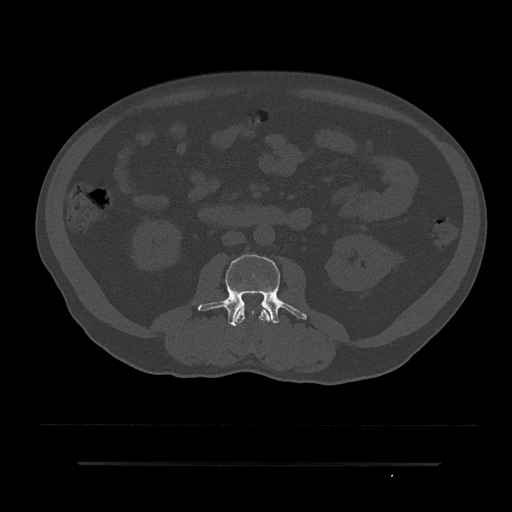
CT including the spine, one axial slice. Reconstruction kernel Br40s/3. 120 kVp. Bone window (W 1800 / L 400 HU). 0.5 mm slice thickness. 512 × 512 image matrix, field of view 464 × 464 mm. Male patient, age 59 years. Case-level facts recorded for this patient, not image findings: primary cancer: bile ducts; vertebrae with lytic lesions (as recorded): T10.
Outlined on this slice (semi-automatically segmented with operator editing):
- L2 vertebra: box from (x=234, y=305) to (x=271, y=324) px
- L3 vertebra: (x=198, y=254)–(x=307, y=326)